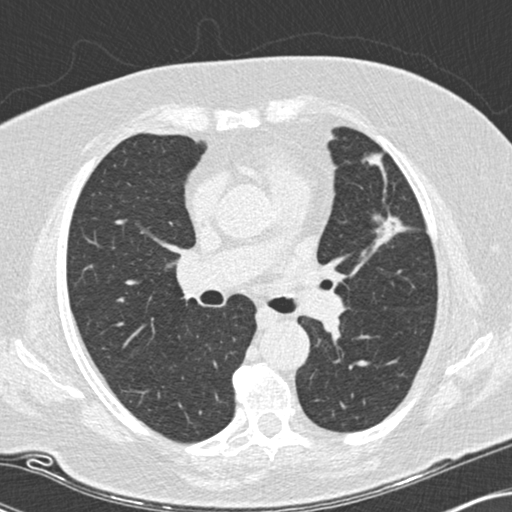
Low-dose screening chest CT, one axial slice. Position 95 of 151 along the scan axis. Lung window (W 1500 / L -600 HU). 2 mm slice thickness. 512 × 512 image matrix, field of view 330 × 330 mm.
Annotated regions visible in this slice (manually delineated by an expert):
- lesion 1 (tumor, upper lobe of left lung): bounding box <373,215,406,247> (left, top, right, bottom; pixels)